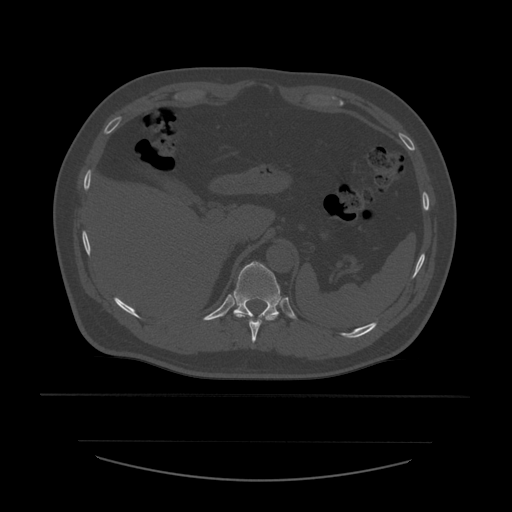
CT including the spine, one axial slice. Slice 284 of 532 in the series (ordered by position). Bone window (W 1800 / L 400 HU). 1.25 mm slice thickness. 512 × 512 image matrix, field of view 441 × 441 mm. Patient age 44 years. Case-level facts recorded for this patient, not image findings: primary cancer: soft tissue sarcoma.
Outlined on this slice (semi-automatic segmentation, software-assisted and operator-edited):
- T10 vertebra: bounding box (x1, y1, x2, y2) in pixels: (236, 315, 278, 343)
- T11 vertebra: (233, 262, 282, 319)